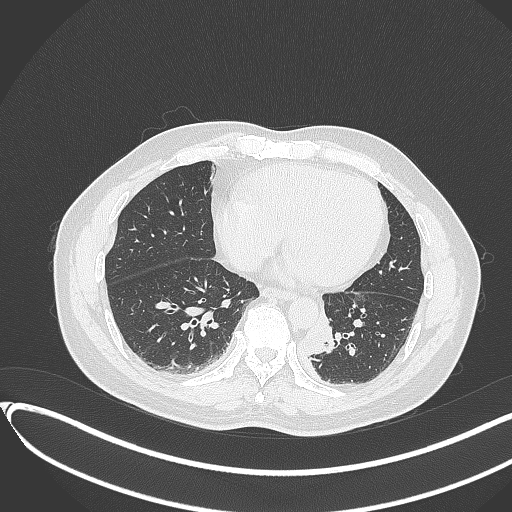
Chest CT, one axial slice; slice 113 of 417 in the series (ordered by position); reconstruction kernel B70f; 120 kVp; lung window (W 1500 / L -600 HU); 1 mm slice thickness; 512 × 512 image matrix, field of view 400 × 400 mm. Patient: male, 54 years. Case-level facts recorded for this patient, not image findings: clinical TNM (as recorded): T3 N0 M0.
Outlined on this slice (rectangle marked by the reading radiologist):
- lung tumour (recorded histology: squamous cell carcinoma): bounding box <302,308,341,361> (left, top, right, bottom; pixels)